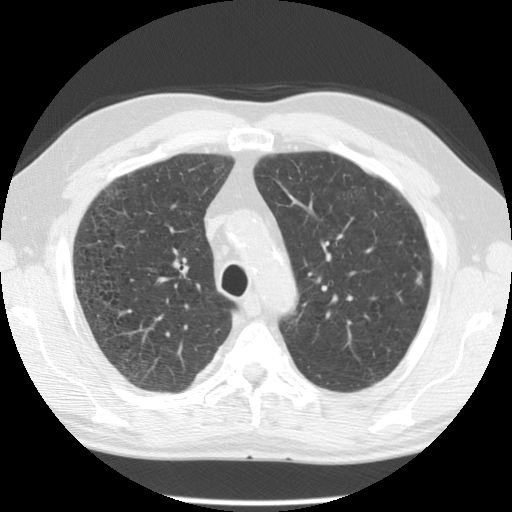
Low-dose screening chest CT, axial slice; baseline annual screen; lung window (W 1500 / L -600 HU); standard (soft-tissue) reconstruction kernel (STANDARD); 120 kVp; 512 × 512 image matrix, field of view 330 × 330 mm. Male, age 59 years at enrolment. Current smoker at enrolment.
- Lesion marked by an expert reader, box from (x=400, y=261) to (x=436, y=300) px.
- The screening reader recorded 2 non-calcified nodules or masses ≥4 mm on this exam; which of them this box marks is not recorded.
- Later outcome: lung cancer diagnosed 436 days after this screen — squamous cell carcinoma, NOS, left upper lobe, poorly differentiated (G3), stage IA (AJCC 6th edition), 10 mm at pathology.